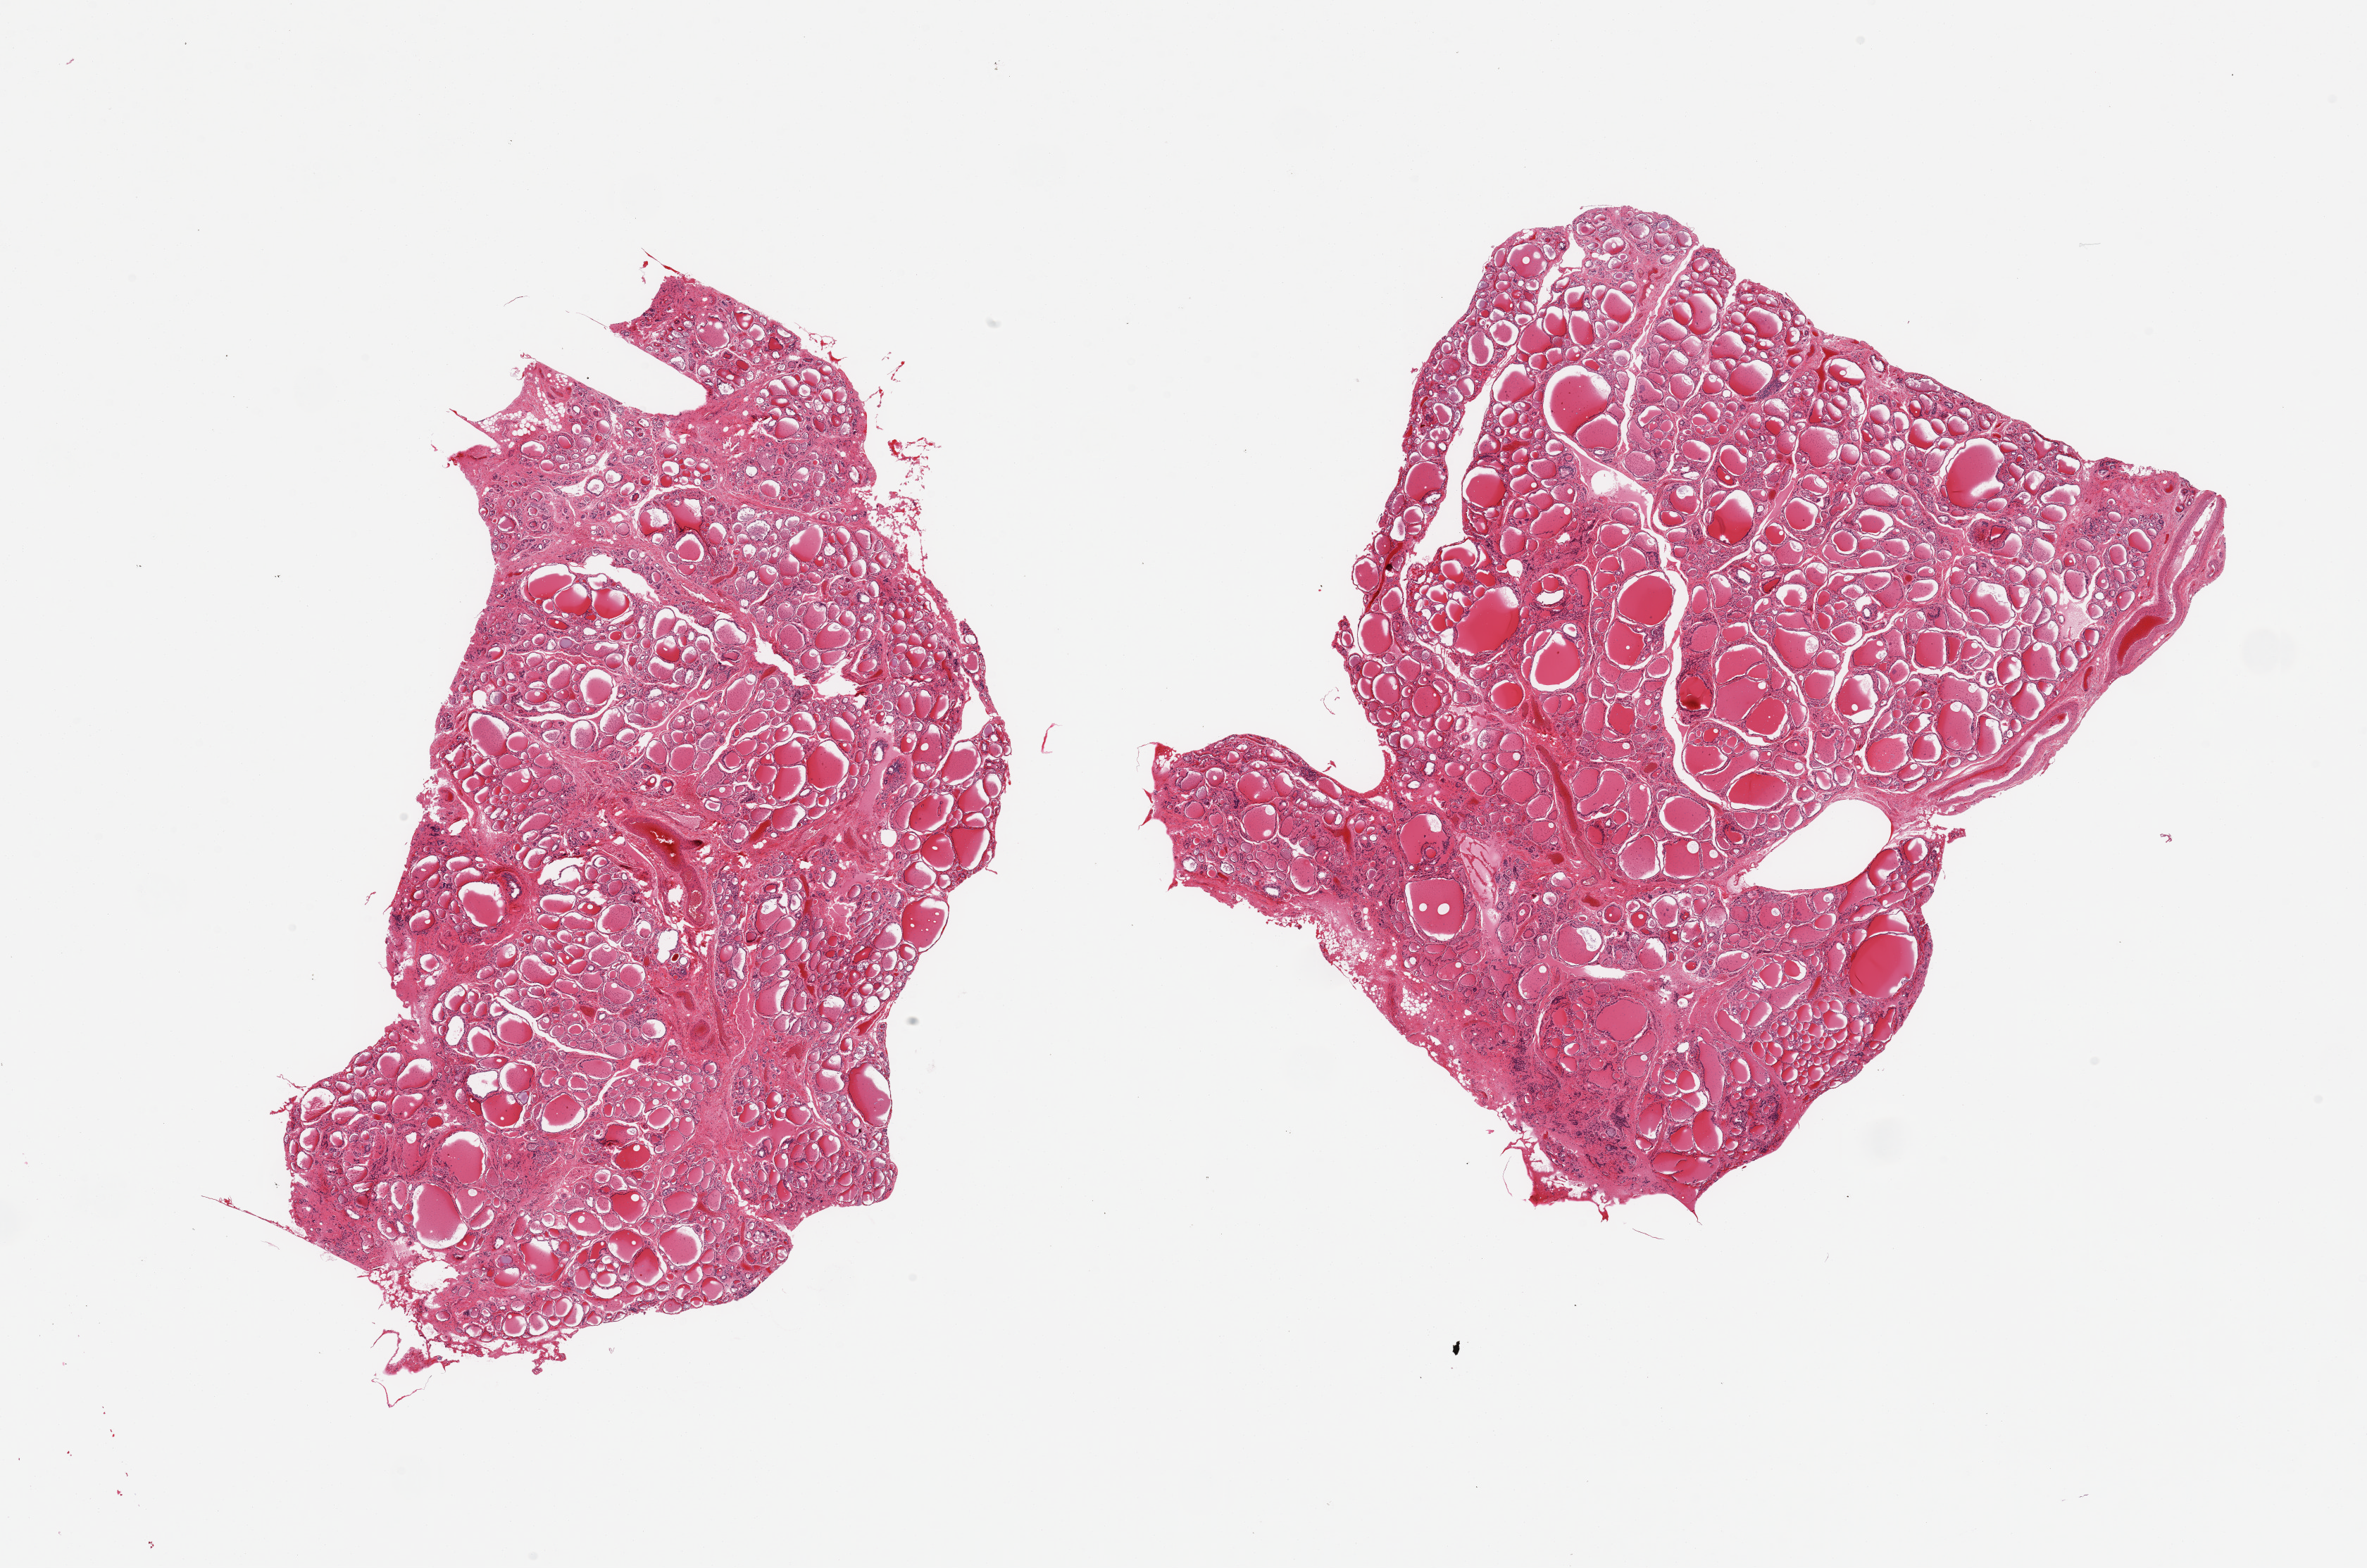
Hematoxylin and eosin (H&E) whole-slide image — shown as a low-resolution overview of the whole scanned area (about 26.6 x 17.6 mm, from a 20x scan); PAXgene-fixed paraffin-embedded (PFPE) section; target tissue: thyroid; tissue donor sample. Donor: male.
Reviewer comment on this tissue sample: 2 pieces, early multinodular goiter.